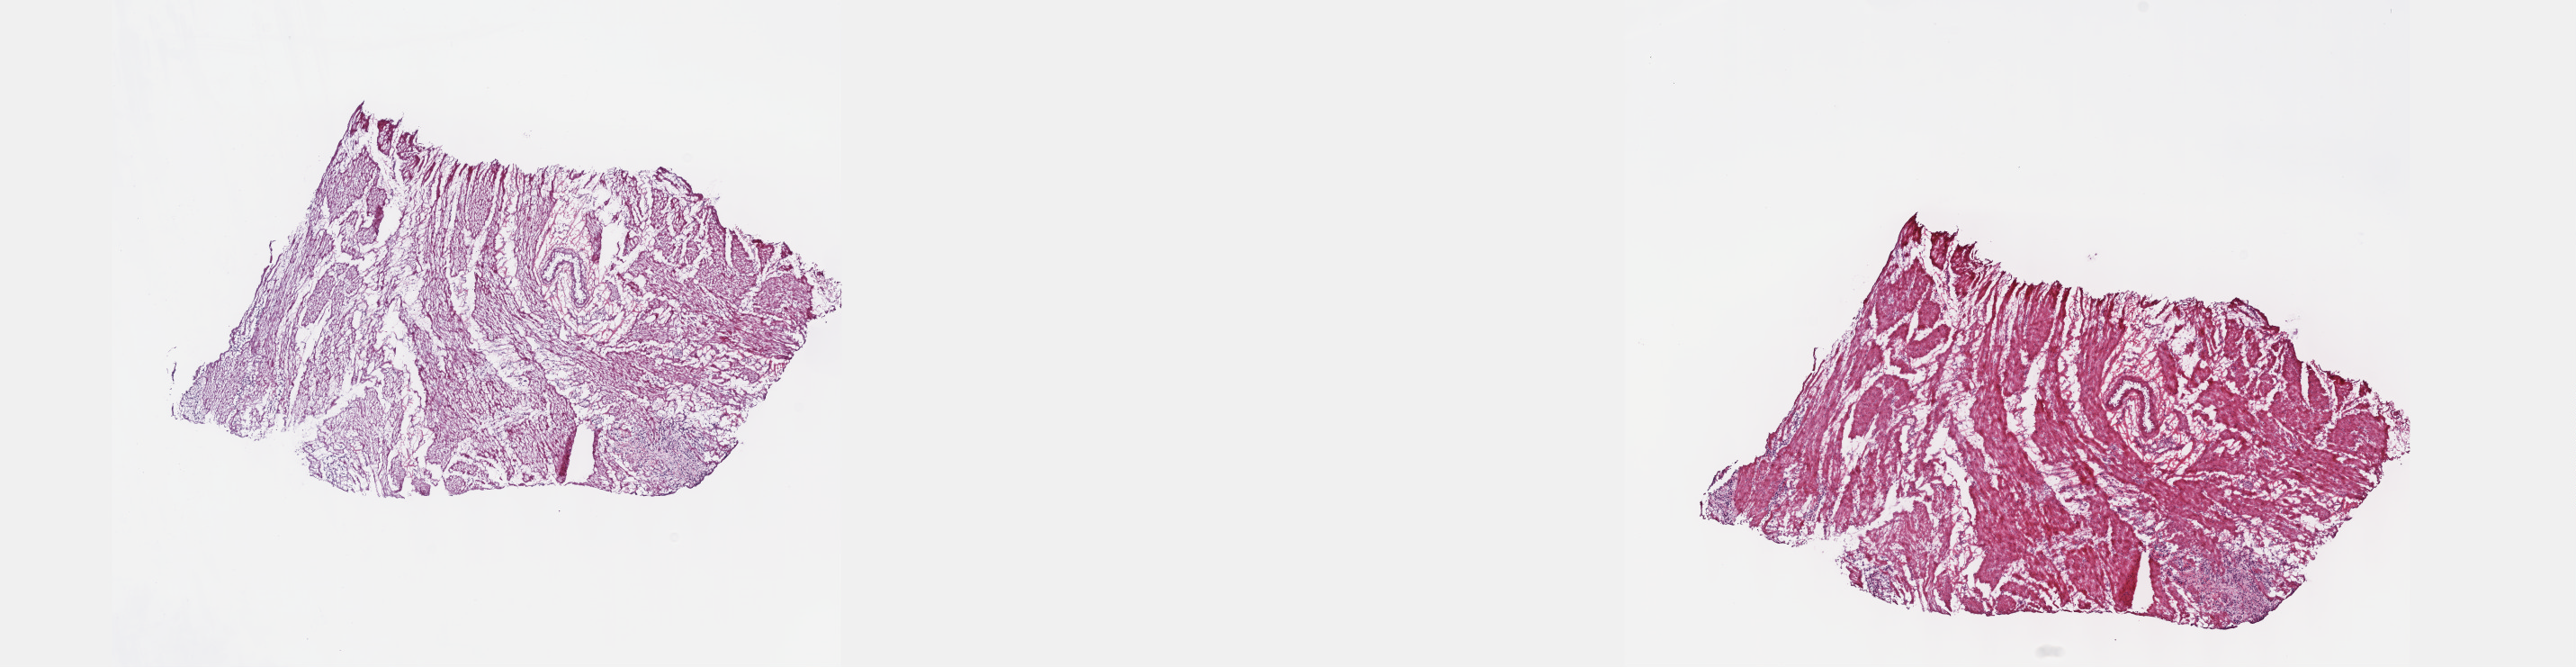
Whole-slide histology image, H&E, whole scanned area (about 23.1 x 6.0 mm) shown as a low-resolution overview; frozen section from the top of the tissue portion; stomach, primary tumour sample. Female, age 58 years at initial diagnosis. Histologic grade: G3 (poorly differentiated). Composition of this section per pathologist review: tumour cells 5%, tumour nuclei 5%, normal cells 95%, stromal cells 0%, necrosis 0%. Infiltration values recorded for this section: lymphocyte infiltration 4%, monocyte infiltration 0%, neutrophil infiltration 0%.
TNM: T3 N1 M0. AJCC pathologic stage: IIIA (6th edition). Lymph nodes positive (case pathology): 3 of 7 examined. Pathologic diagnosis: Carcinoma, diffuse type.